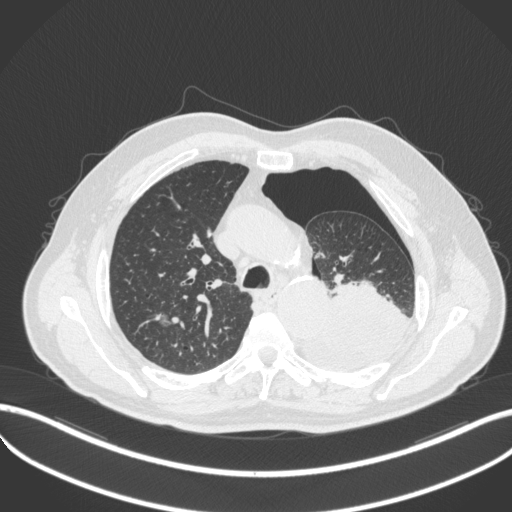
Chest CT, one axial slice. Position 365 of 466 along the scan axis. Reconstruction kernel B31f. 120 kVp. Lung window (W 1500 / L -600 HU). 1 mm slice thickness. 512 × 512 image matrix. Patient: male, 76 years. From the clinical record (not read from this slice): clinical TNM (as recorded): T3 N0 M1b.
Outlined on this slice (bounding box drawn by a radiologist):
- lung tumour (recorded histology: adenocarcinoma): box from (x=304, y=279) to (x=415, y=371) px